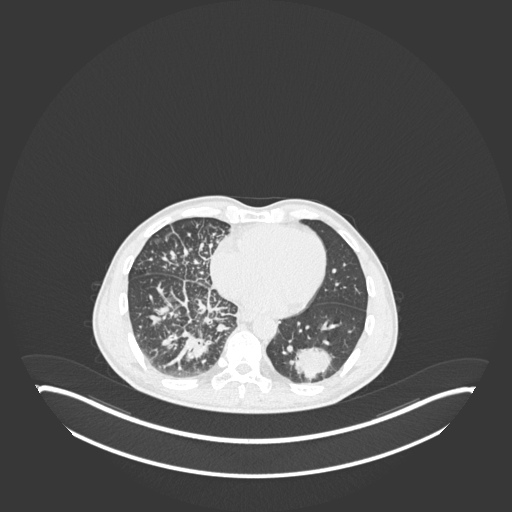
Chest CT, one axial slice; slice 79 of 237 in the series (ordered by position); lung window (W 1500 / L -600 HU); 1 mm slice thickness; 512 × 512 image matrix, field of view 500 × 500 mm. Male patient, age 49 years. Case-level facts recorded for this patient, not image findings: clinical TNM (as recorded): T2b N1 M0.
Structures marked on this image (rectangle marked by the reading radiologist):
- lung tumour (recorded histology: adenocarcinoma): bounding box <290,346,336,382> (left, top, right, bottom; pixels)